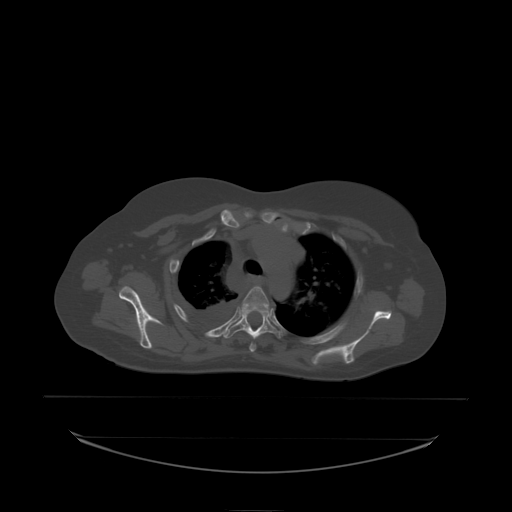
CT including the spine, one axial slice; slice 169 of 242 in the series (ordered by position); bone window (W 1800 / L 400 HU); 512 × 512 image matrix, field of view 500 × 500 mm. Female patient, age 53 years. From the clinical record (not read from this slice): primary cancer: lung.
Outlined on this slice (semi-automatic segmentation, software-assisted and operator-edited):
- T3 vertebra: bounding box [x1, y1, x2, y2] px = [242, 287, 272, 311]
- T4 vertebra: [228, 308, 281, 338]